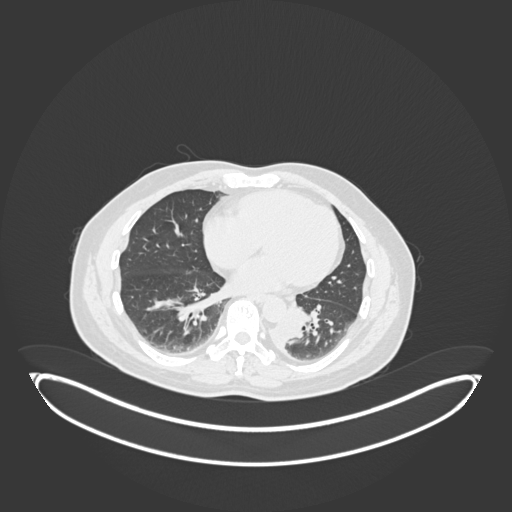
Chest CT, one axial slice; position 68 of 258 along the scan axis; 120 kVp; lung window (W 1500 / L -600 HU); 1 mm slice thickness; 512 × 512 image matrix, field of view 500 × 500 mm. Patient: male, 54 years. From the clinical record (not read from this slice): clinical TNM (as recorded): T3 N0 M0.
Outlined on this slice (rectangle marked by the reading radiologist):
- lung tumour (recorded histology: squamous cell carcinoma): bounding box (x1, y1, x2, y2) in pixels: (271, 317, 307, 354)